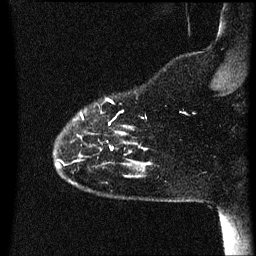
Breast MRI (dynamic contrast-enhanced), one sagittal slice; slice 9 of 60 in the series (ordered by position); dynamic contrast-enhanced series, image 2 of 3 at this slice position (ordered by acquisition); 1.5 T; TE 4.2 ms, TR 8.4 ms; 2.2 mm slice thickness; 256 × 256 image matrix. Patient: female, 35 years. Case-level facts recorded for this patient, not image findings: setting: breast cancer imaged before/during neoadjuvant chemotherapy; receptor status: HER2-positive.
Annotated regions visible in this slice (semi-automatic segmentation, software-assisted and operator-edited):
- analysis volume of interest (the breast-tissue region the enhancement analysis was run in; not a lesion): box from (x=55, y=98) to (x=153, y=173) px
- tumour enhancement mask (voxels above the 70 % enhancement threshold inside the analysis volume of interest): (x=81, y=114)–(x=133, y=151)